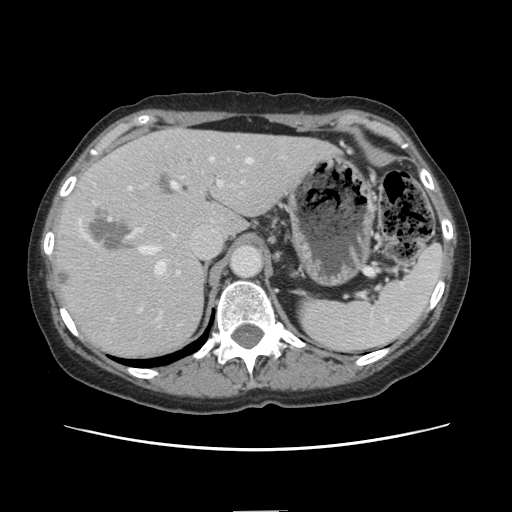
Contrast-enhanced abdominal CT, one axial slice. Position 100 of 141 along the scan axis. 120 kVp. Intravenous contrast given. Soft-tissue window (W 400 / L 40 HU). 2.5 mm slice thickness. 512 × 512 image matrix. Female patient, age 63 years. Case-level facts recorded for this patient, not image findings: diagnosis: colorectal cancer liver metastases, imaged before liver resection; multiple liver metastases: yes; largest metastasis: 3.2 cm.
Annotated regions visible in this slice (outlined manually by an expert reader):
- hepatic veins: box from (x=141, y=158) to (x=252, y=274) px
- liver: (x=52, y=130)–(x=333, y=359)
- planned liver remnant (the part of the liver to remain after resection): (x=185, y=130)–(x=334, y=238)
- portal vein (with intrahepatic branches): (x=127, y=180)–(x=223, y=273)